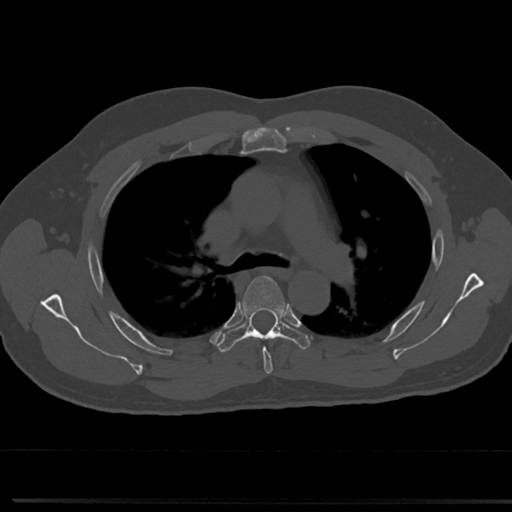
CT including the spine, one axial slice. Position 513 of 817 along the scan axis. Bone window (W 1800 / L 400 HU). 512 × 512 image matrix. Patient: male, 61 years. From the clinical record (not read from this slice): primary cancer: prostate.
Structures marked on this image (semi-automatically segmented with operator editing):
- T4 vertebra: bounding box [x1, y1, x2, y2] px = [246, 276, 281, 372]
- T5 vertebra: [219, 276, 310, 352]